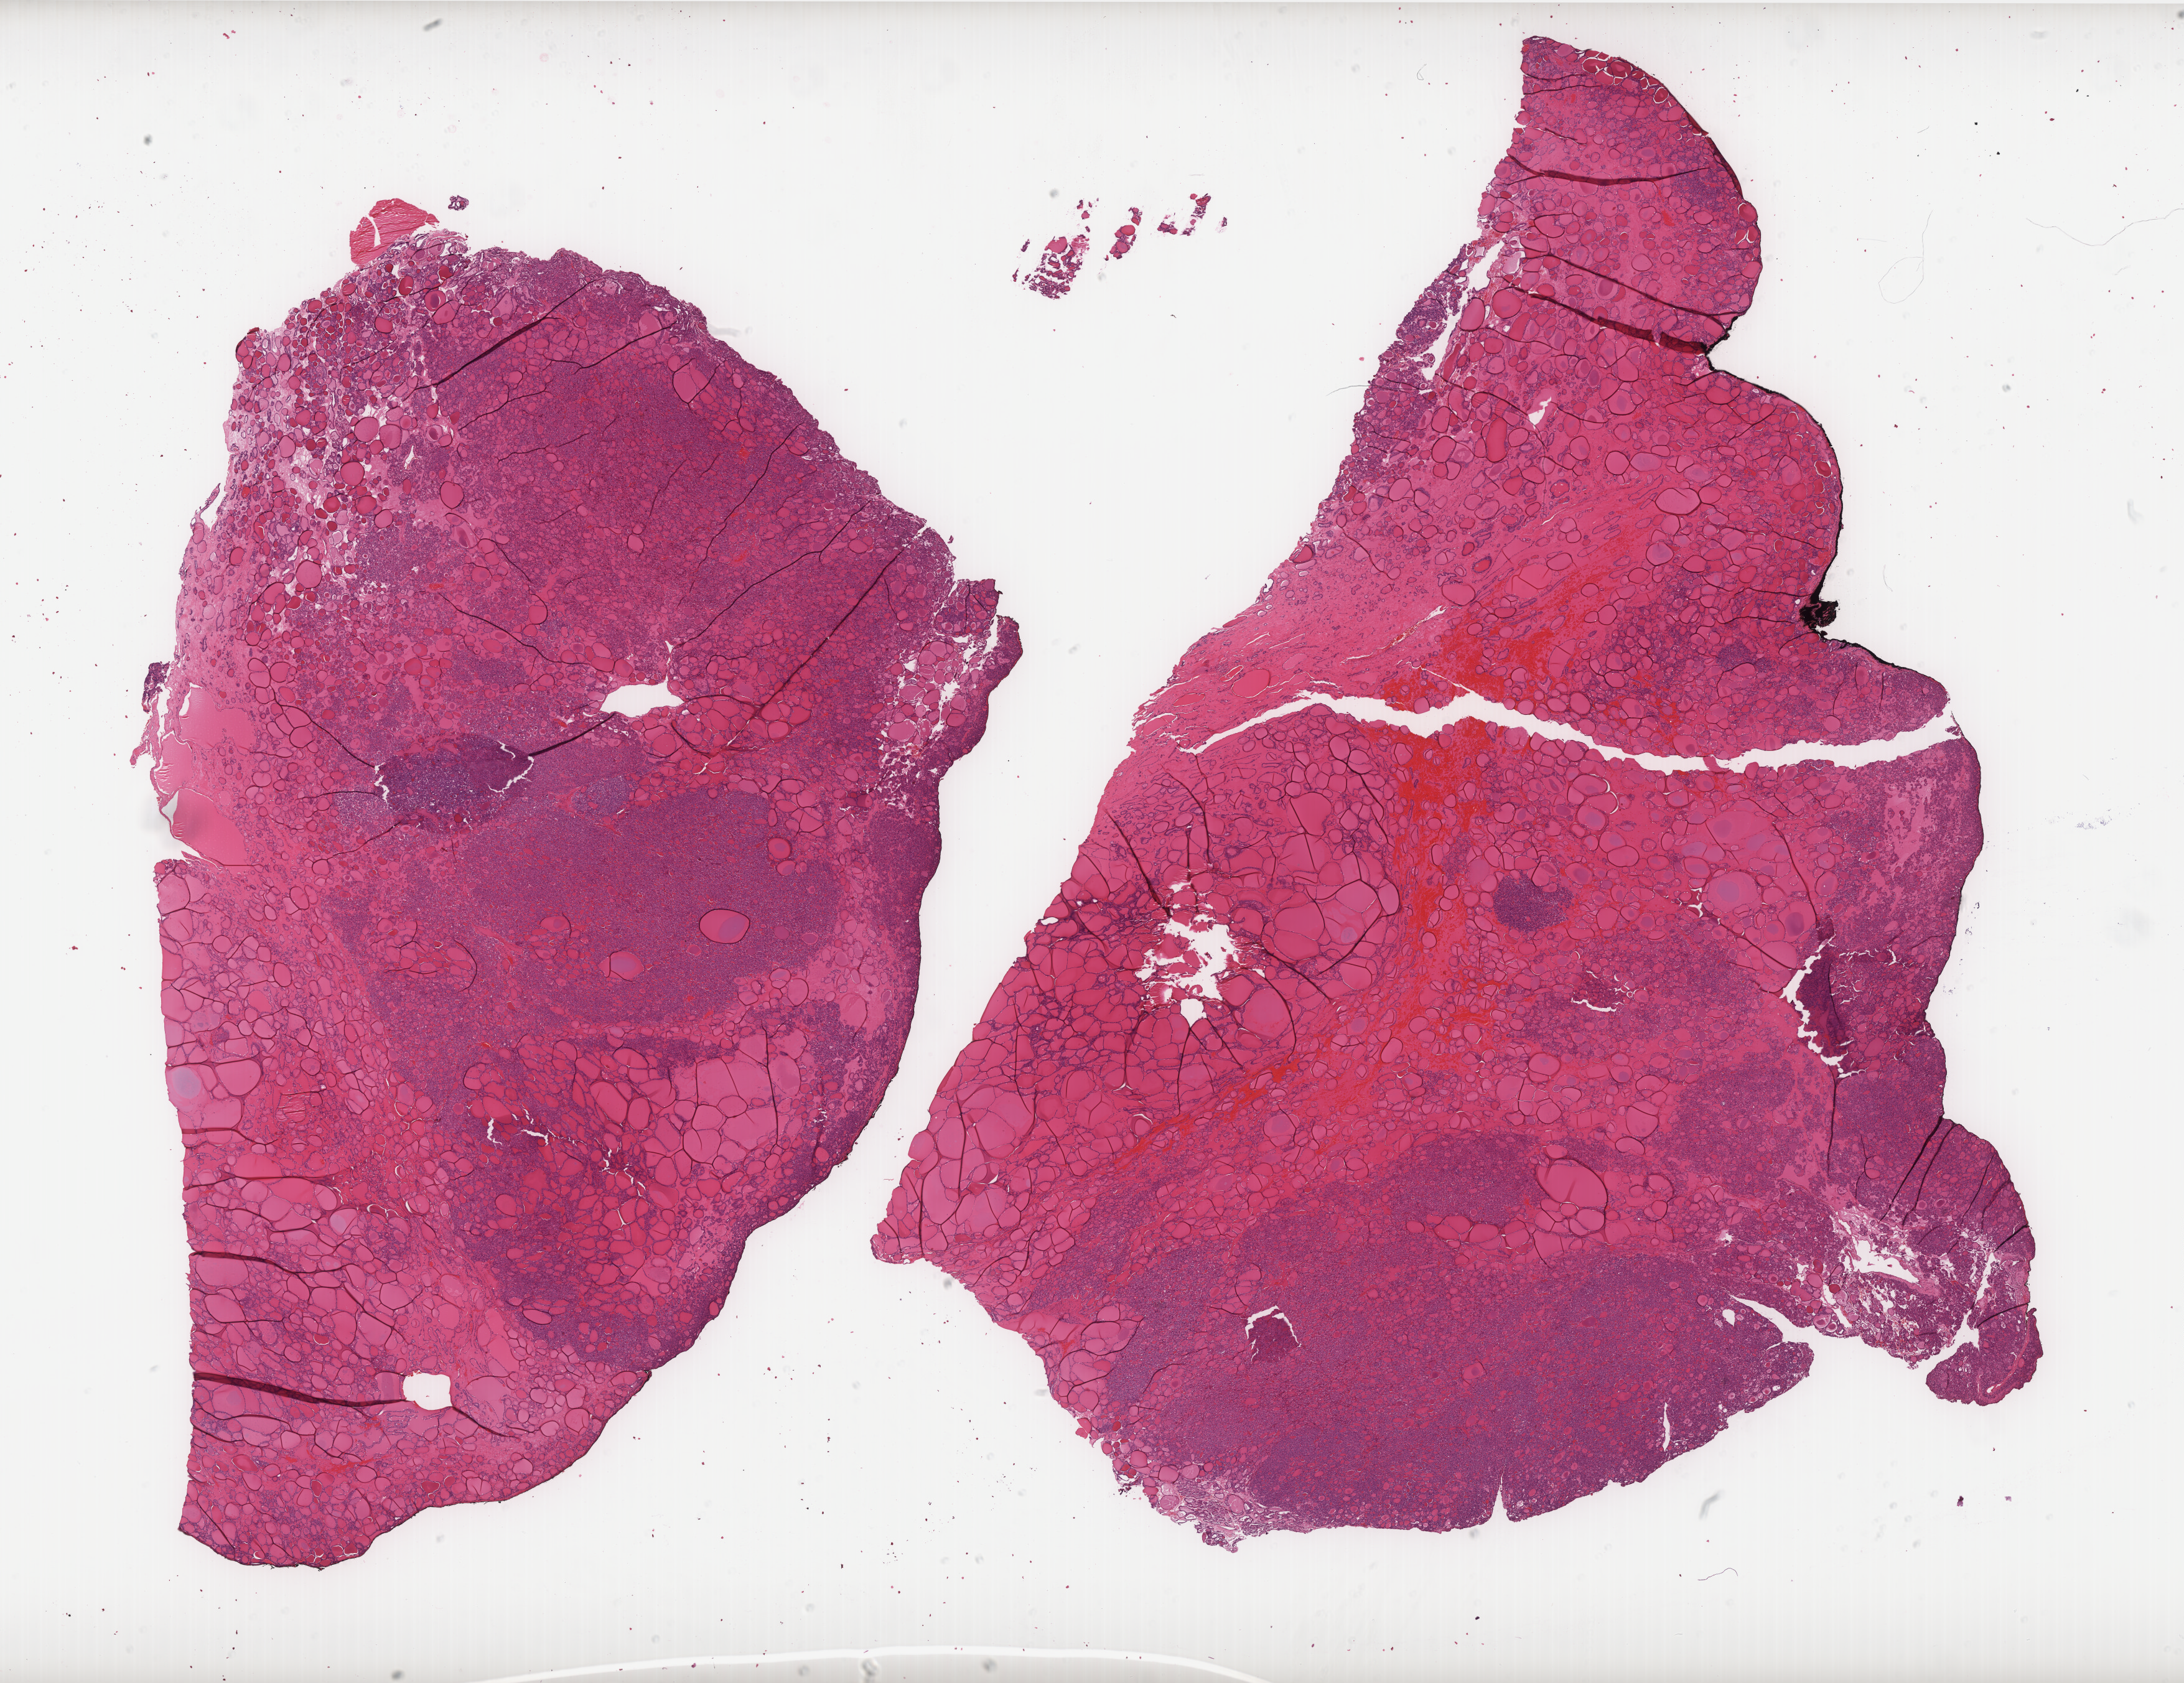
Digitized H&E tissue section (whole slide) — low-resolution overview of the scanned area, about 28.1 x 21.7 mm; formalin-fixed paraffin-embedded (FFPE) diagnostic section; primary tumour sample from the thyroid. Patient: female, age at initial diagnosis 63 years.
Diagnosis: Papillary adenocarcinoma, NOS (thyroid gland).